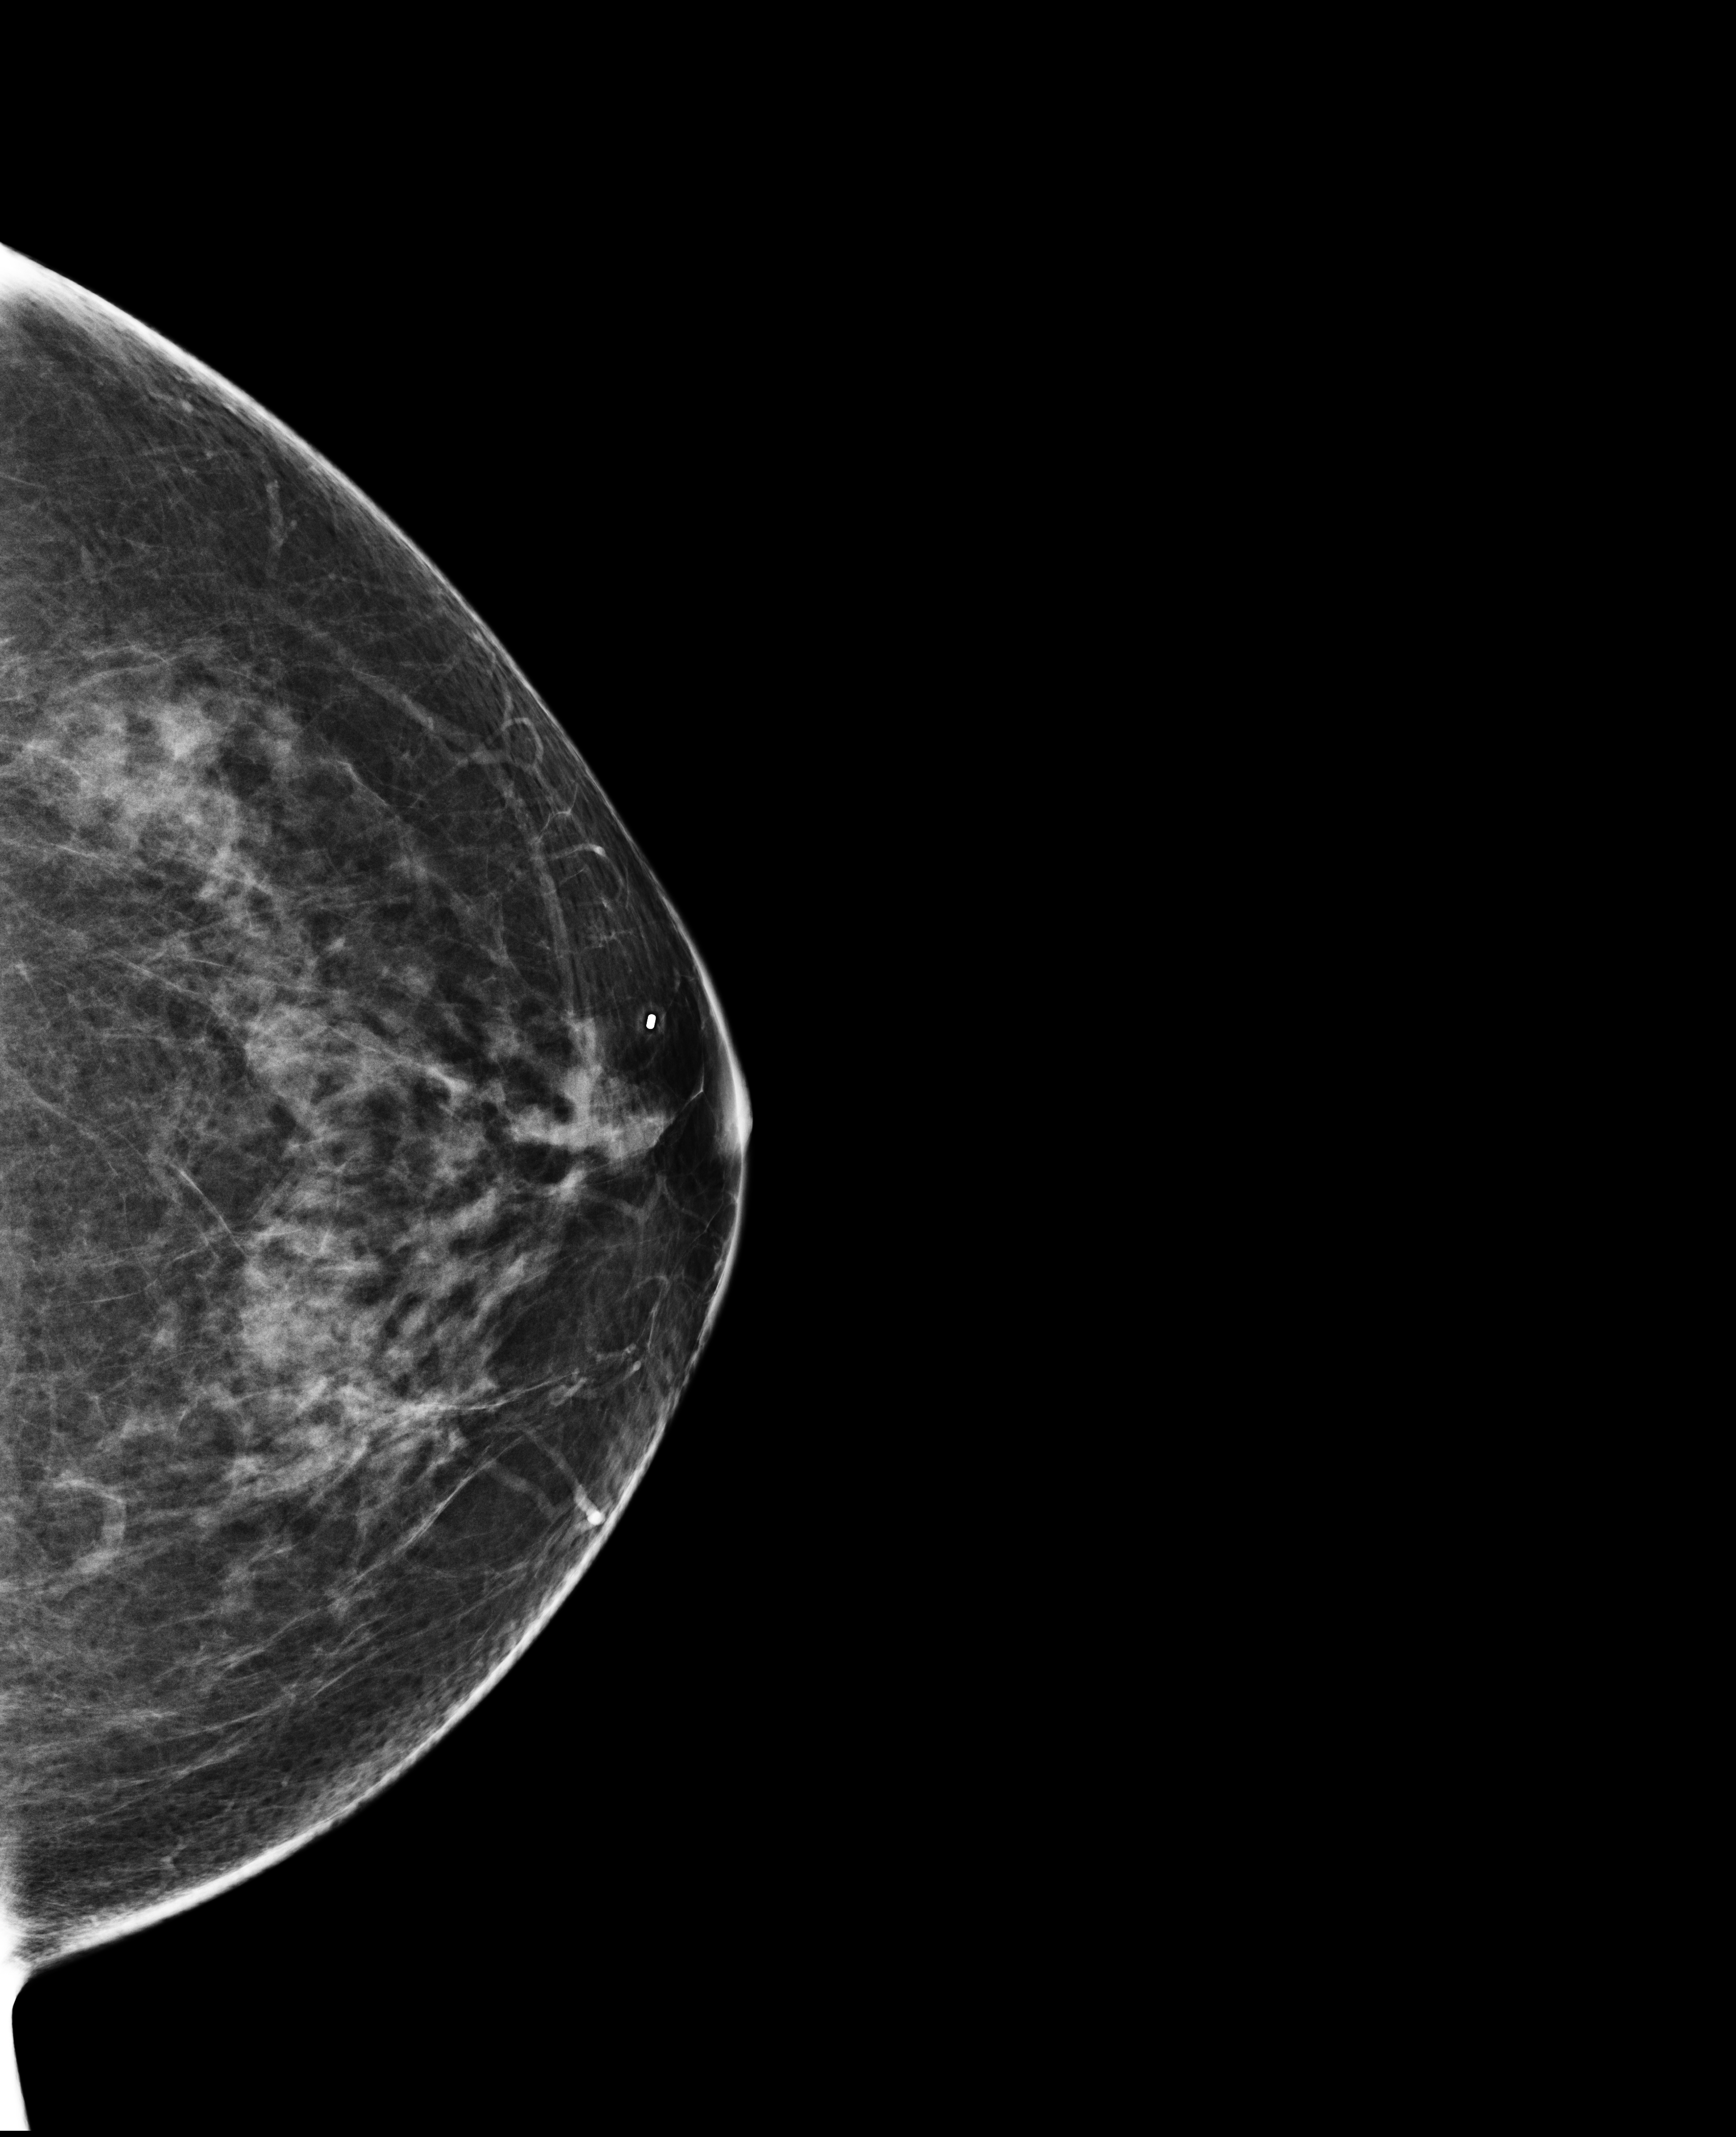
Screening examination. Patient: female, 57 years.
Image type: full-field digital mammogram. Breast: left. Projection: craniocaudal (CC) view.